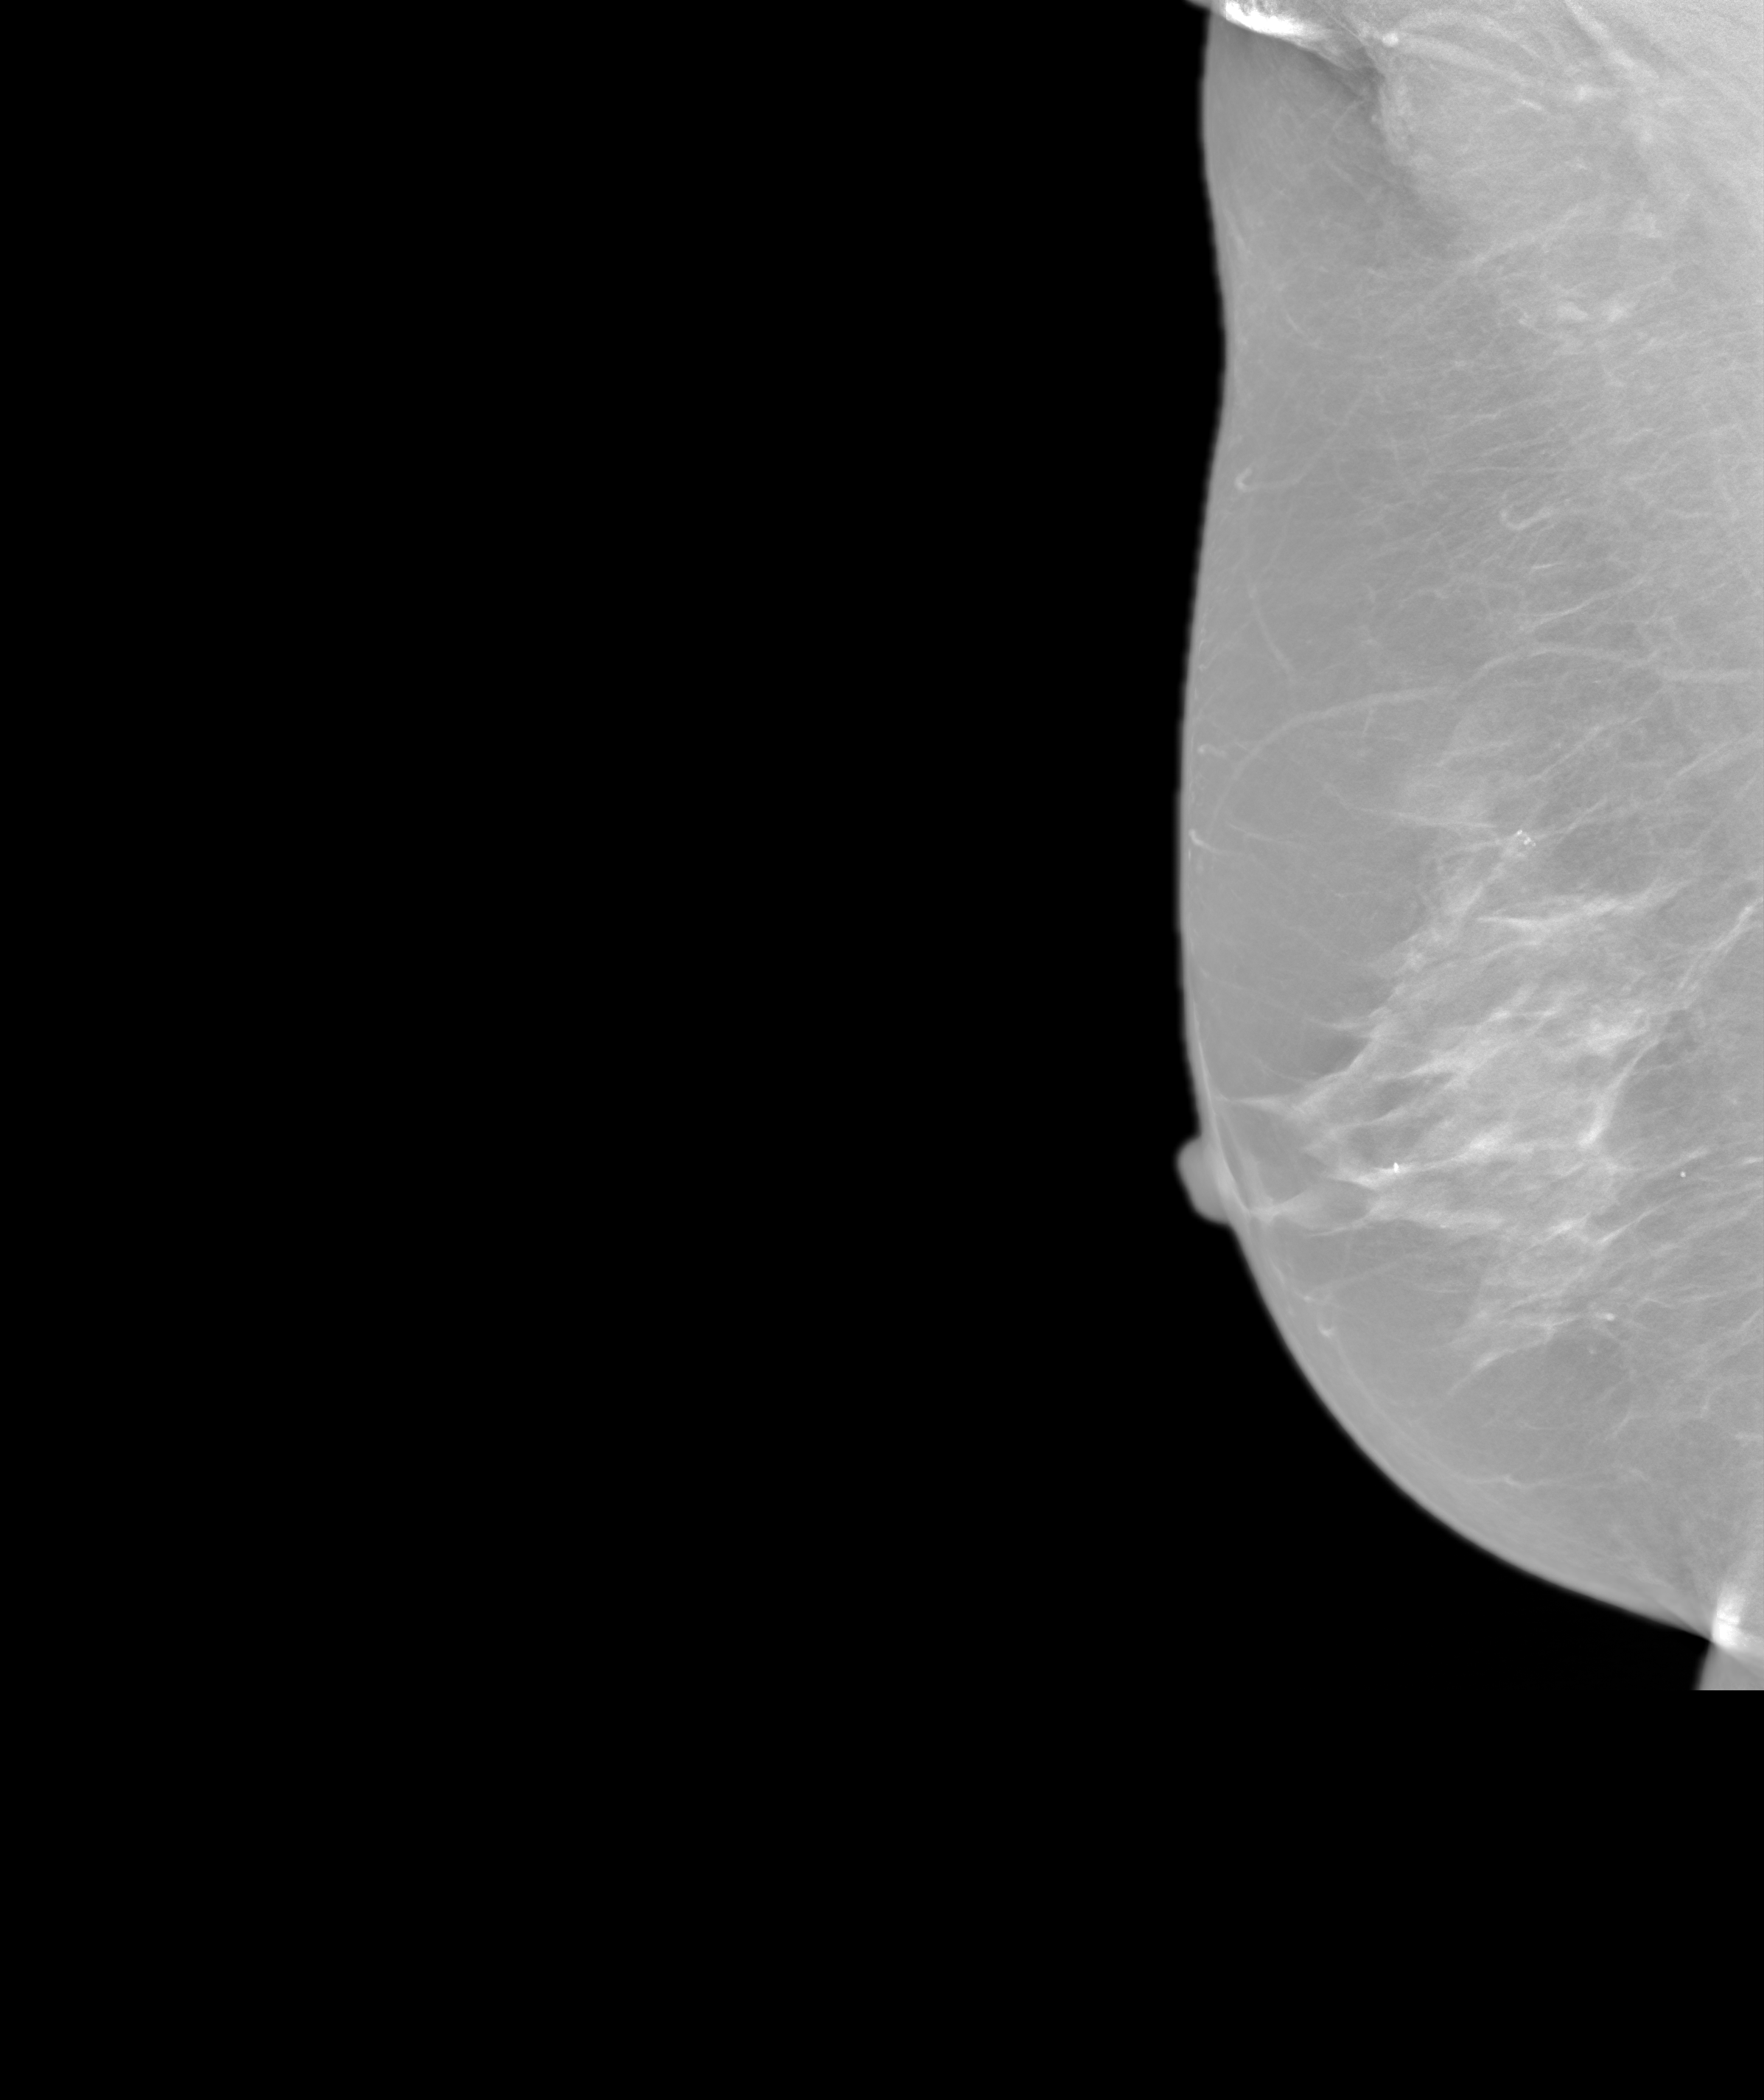
Screening examination, system: SenoIris_1SP1.2(425).
Image type: synthesized 2-D view from tomosynthesis. Breast: right. Projection: mediolateral oblique (MLO) view.